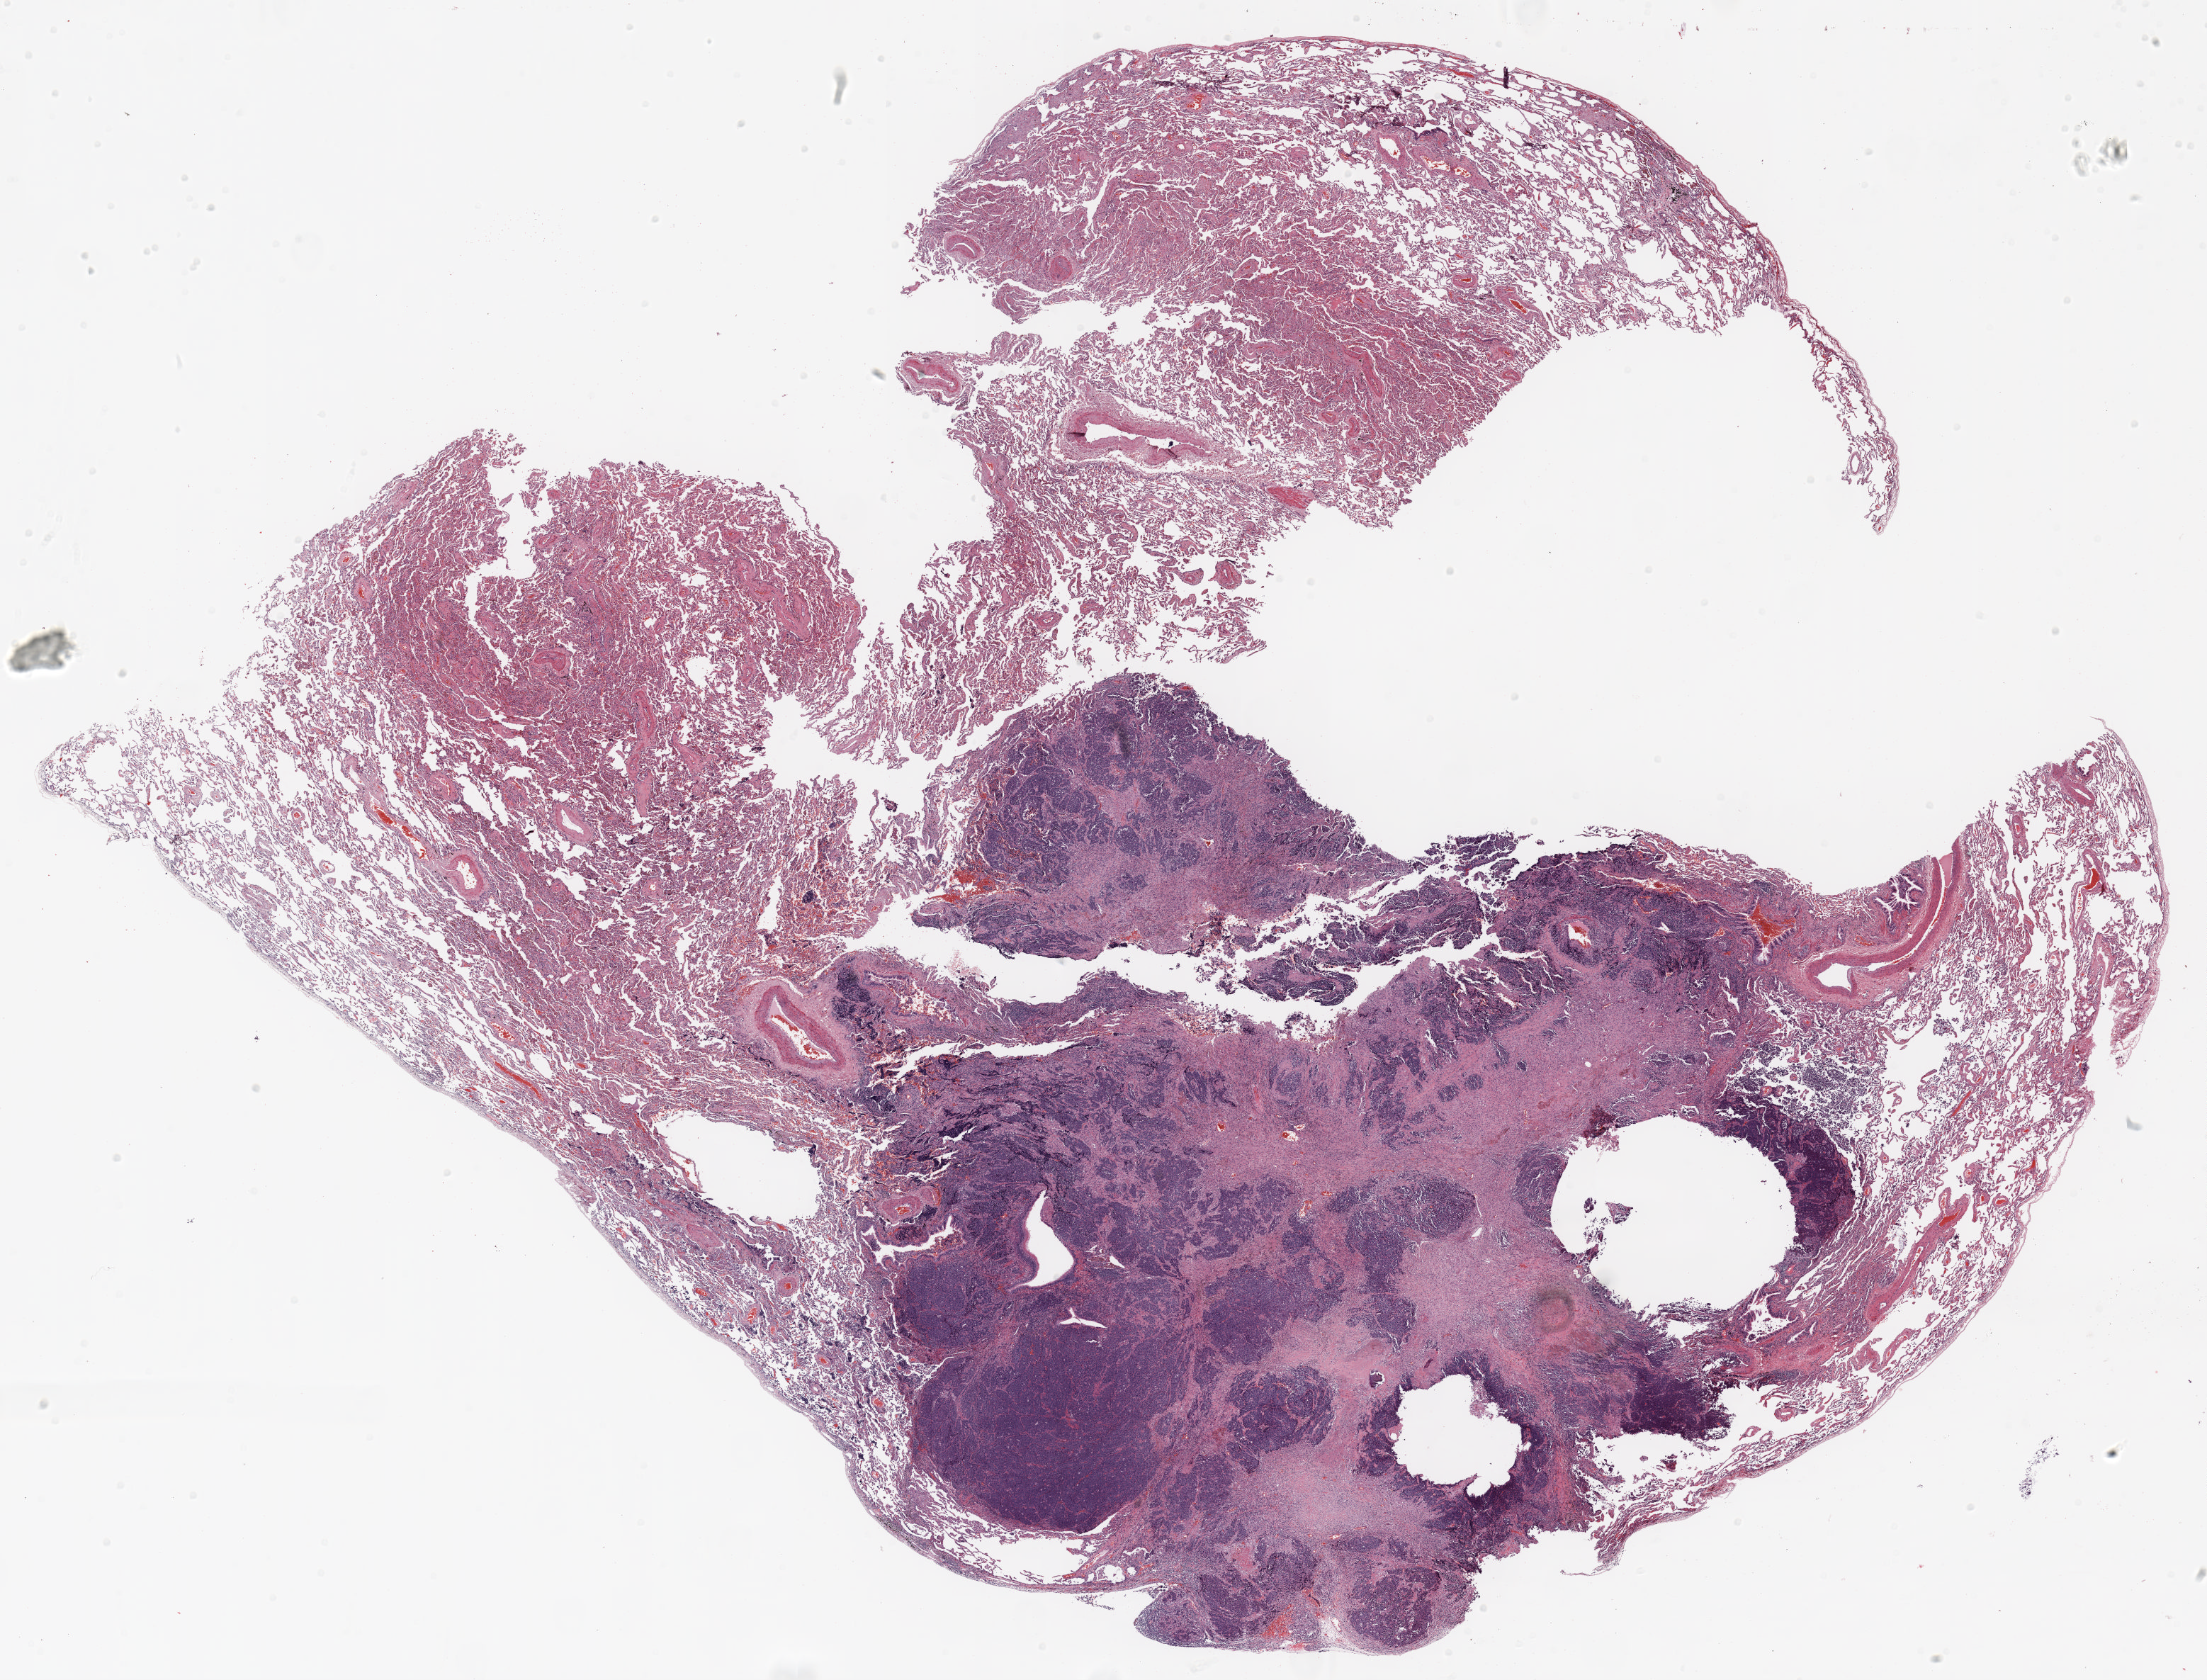
Whole-slide histology image, Hematoxylin and eosin (H&E) stained — a low-resolution overview of the entire scanned area, about 25.0 x 19.0 mm; formalin-fixed paraffin-embedded (FFPE) section; lung. Male, age 69 at enrolment. Former smoker at enrolment. Grade: poorly differentiated (G3).
Participant's lung-cancer diagnosis: Large cell neuroendocrine carcinoma (ICD-O-3 8013/3). Primary tumour location (clinical record): right upper lobe. ICD-O-3 topography: upper lobe of lung (C34.1). Stage (AJCC 6th edition): IA. Tumour size (pathology): 23 mm.